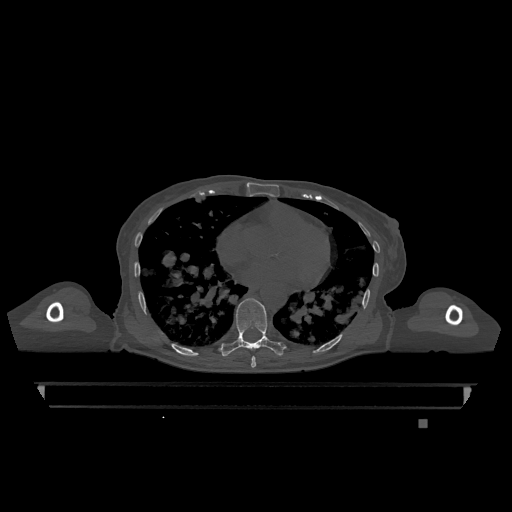
CT including the spine, one axial slice; position 695 of 1317 along the scan axis; bone window (W 1800 / L 400 HU); 512 × 512 image matrix, field of view 500 × 500 mm. Patient: female, 74 years. From the clinical record (not read from this slice): primary cancer: lung.
Annotated regions visible in this slice (semi-automatic segmentation, software-assisted and operator-edited):
- T7 vertebra: bounding box <251,356,256,368> (left, top, right, bottom; pixels)
- T9 vertebra: <221,298,284,357>